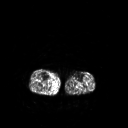
FDG PET of an extremity soft-tissue mass (from a PET/CT study), one axial slice. Slice 120 of 267 in the series (ordered by position). 3.27 mm slice thickness. 128 × 128 image matrix. Patient: male, 69 years. From the clinical record (not read from this slice): histological type: pleiomorphic liposarcoma; grade: high; site of the primary tumour: right calf.
Outlined on this slice (expert contour drawn on MRI and transferred to this co-registered scan by the dataset authors):
- gross tumour volume including surrounding oedema: box from (x=53, y=84) to (x=55, y=86) px